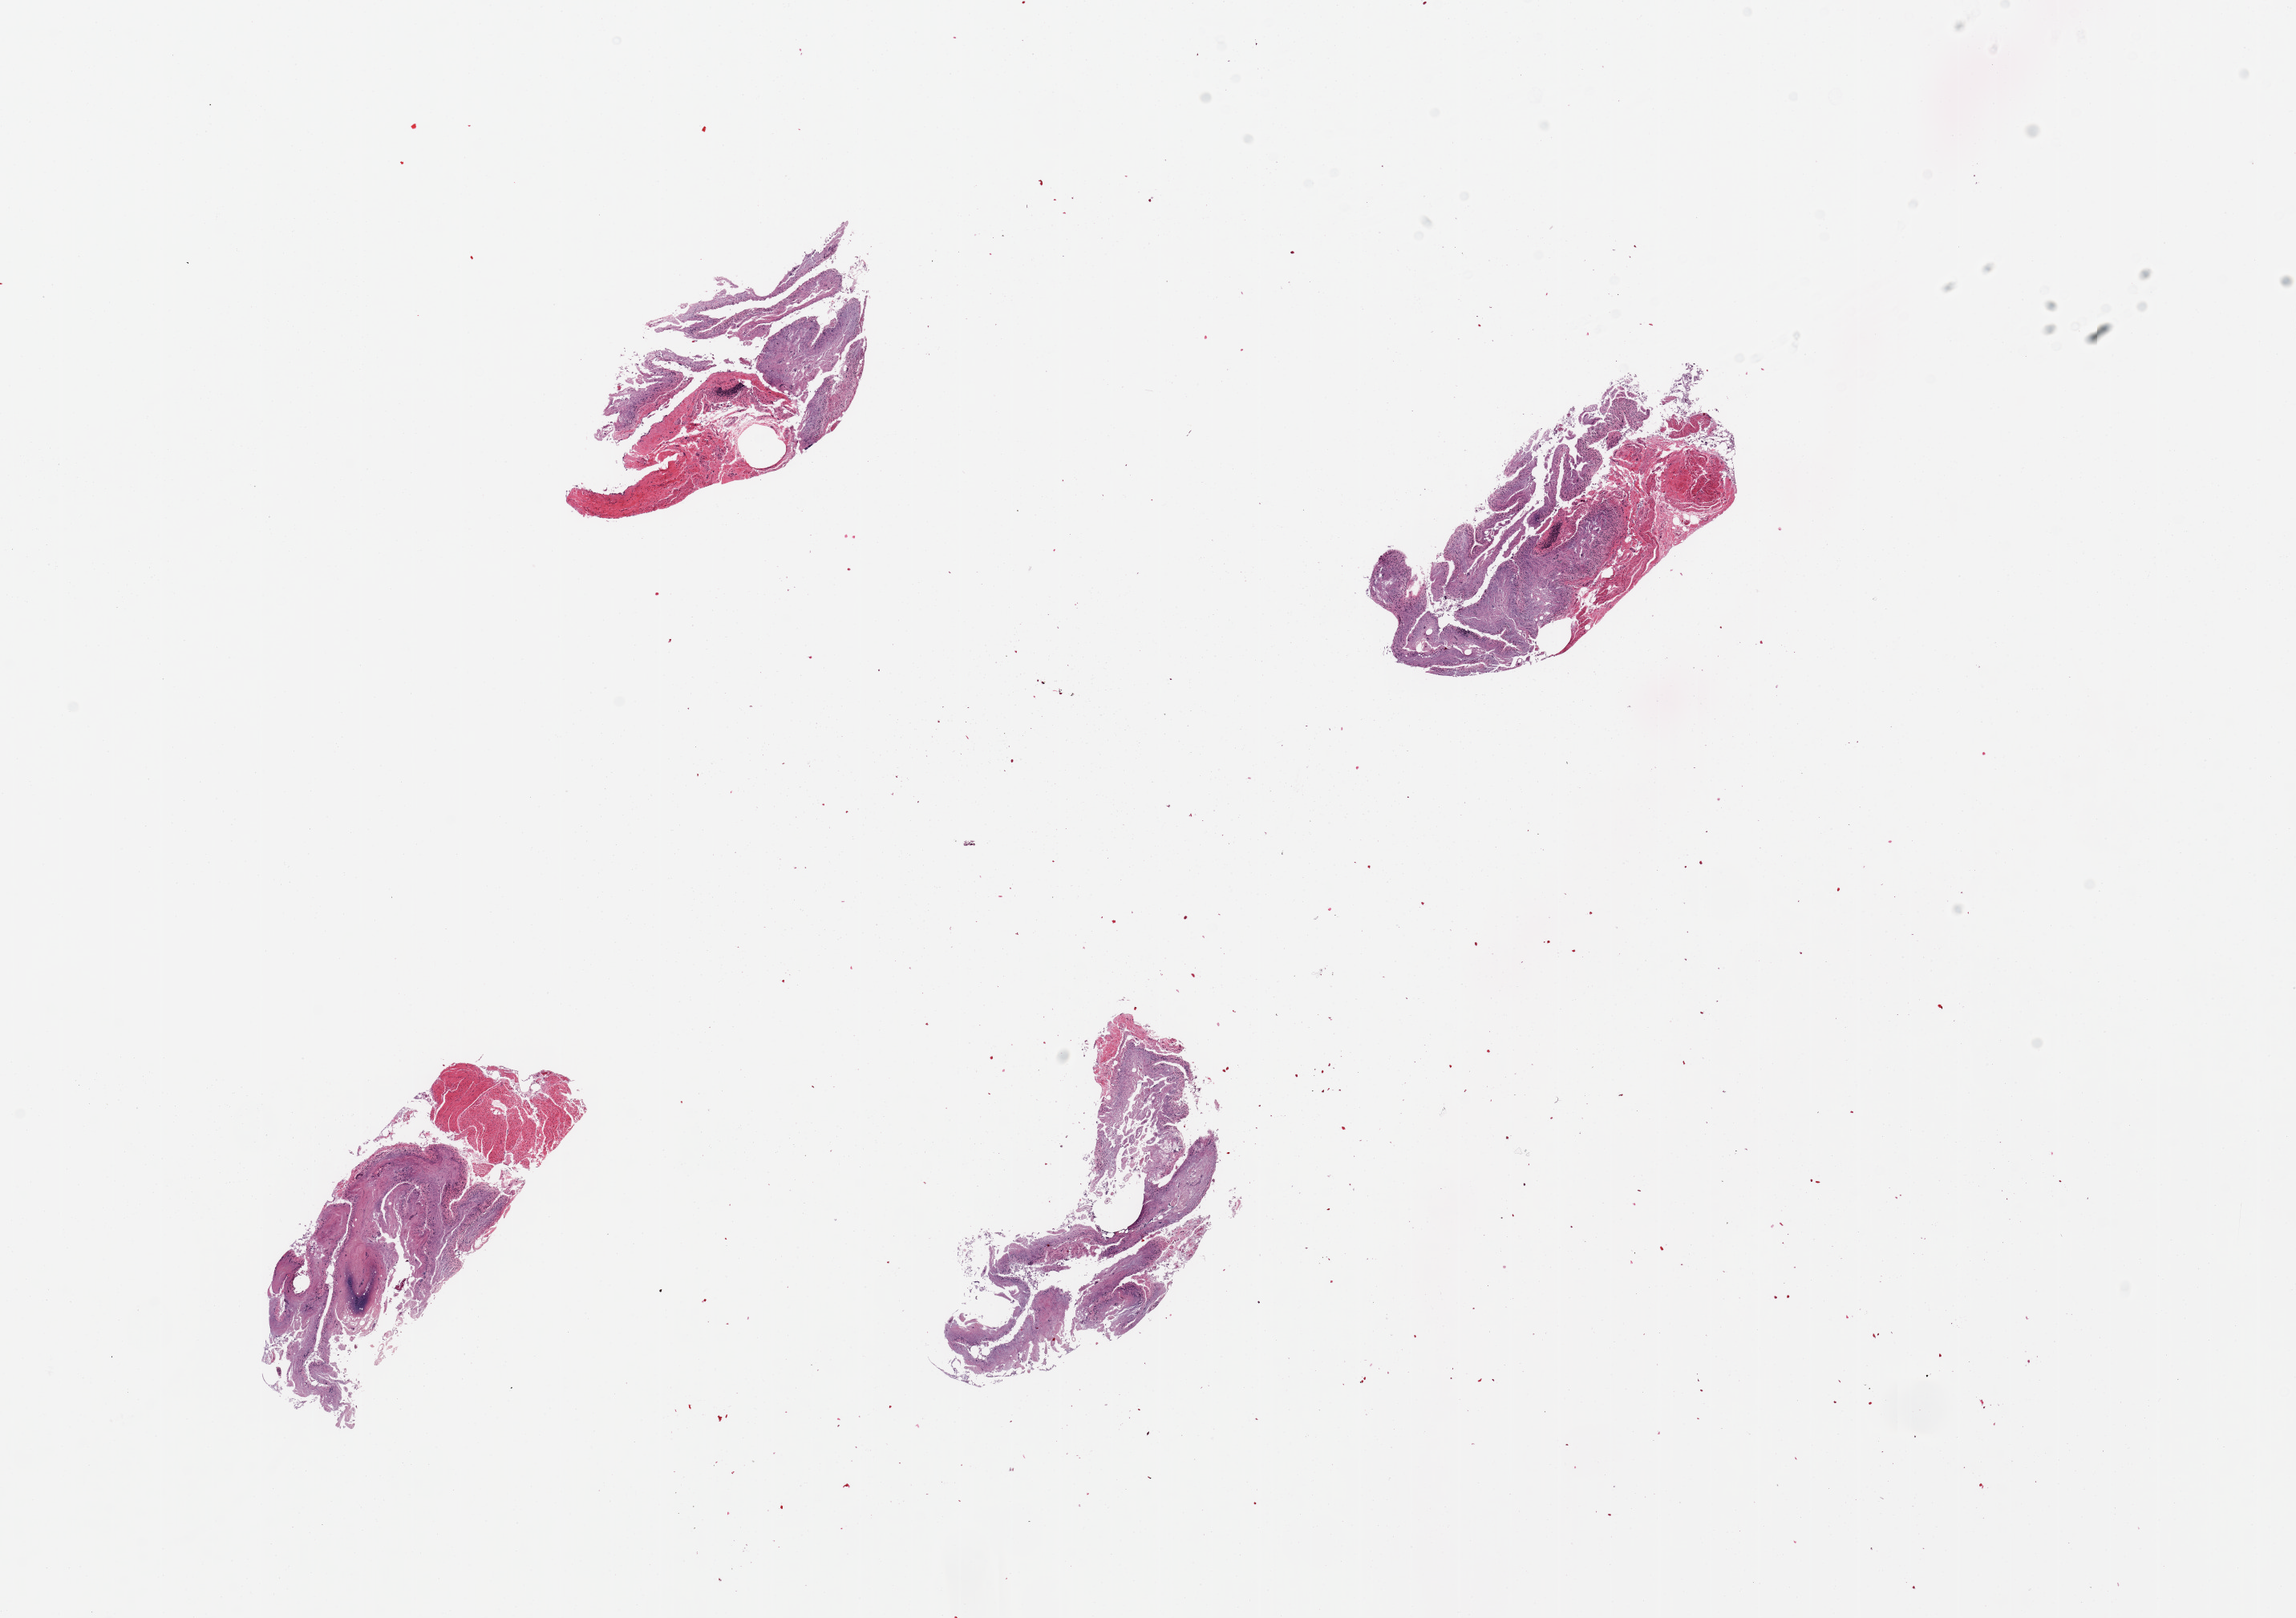
Whole-slide image, hematoxylin and eosin (H&E) stain, brightfield — whole scanned area (about 22.6 x 16.0 mm) shown as a low-resolution overview, PAXgene-fixed paraffin-embedded (PFPE) section, target tissue: ileum, donor tissue sample.
Pathologist's review note for this sample: 4 pieces, fragmented muscularis and severely autolyzed mucosa, no residual lymphoid tissue.